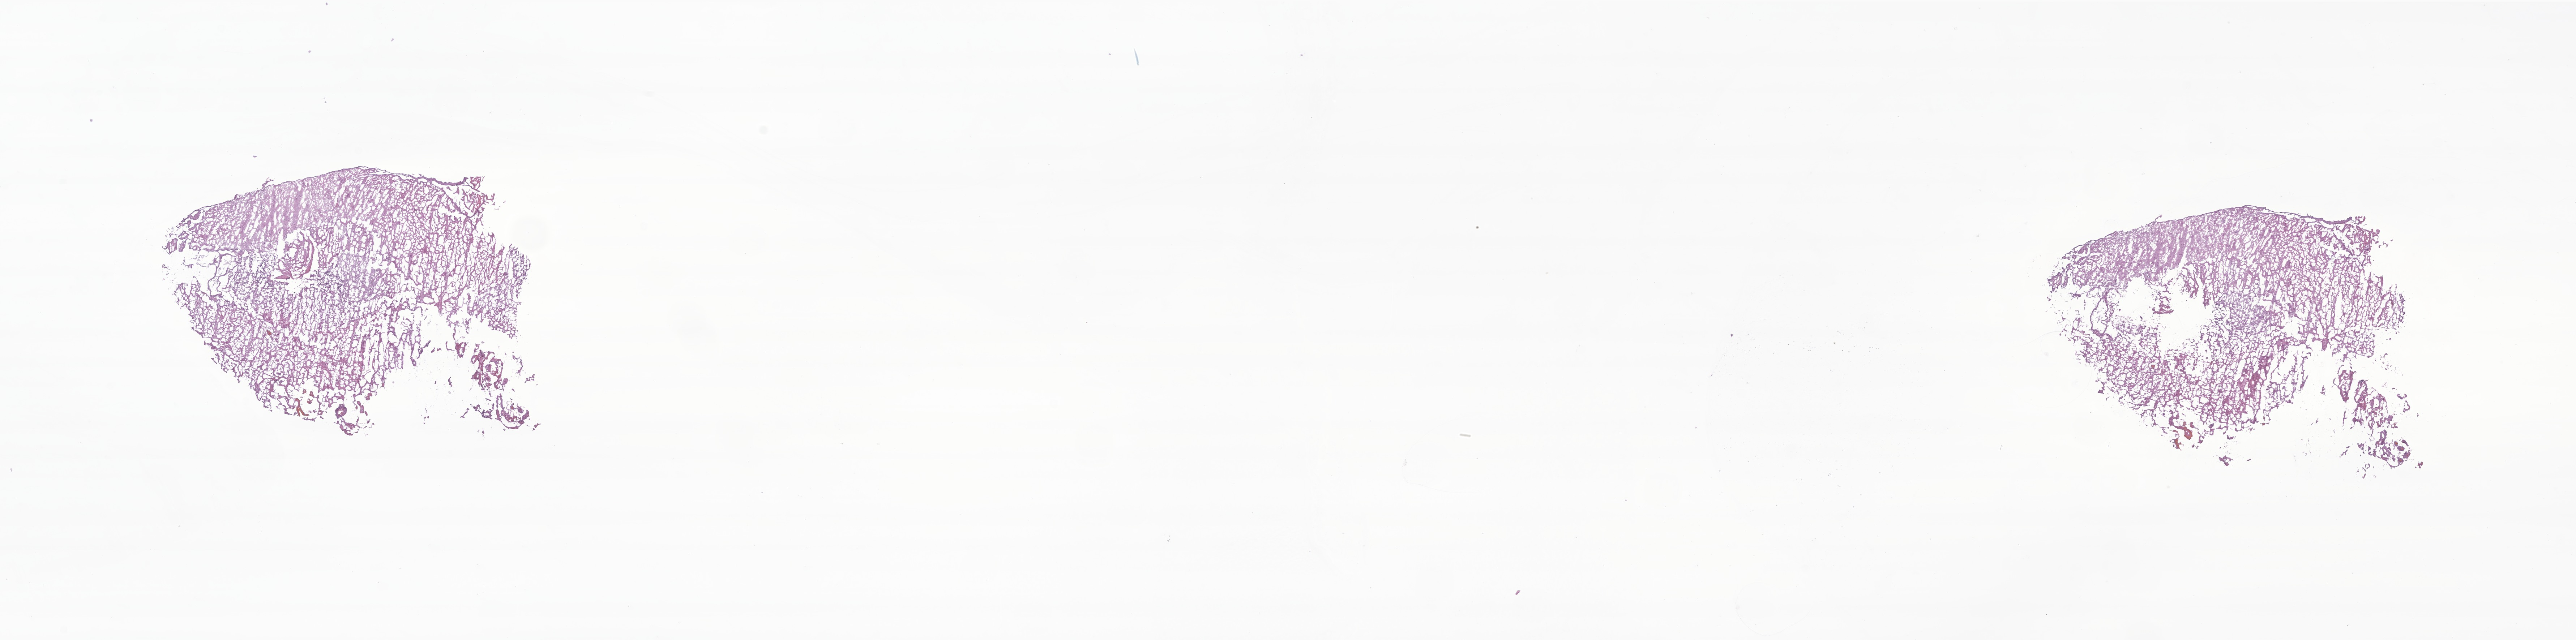
Whole-slide image, haematoxylin and eosin stain of tumor tissue from the brain, a low-resolution overview of the entire scanned area, about 30.0 x 7.5 mm, frozen section (OCT-embedded). Patient male; age 50 months (4 years 2 months).
* recorded diagnosis: Pilocytic astrocytoma